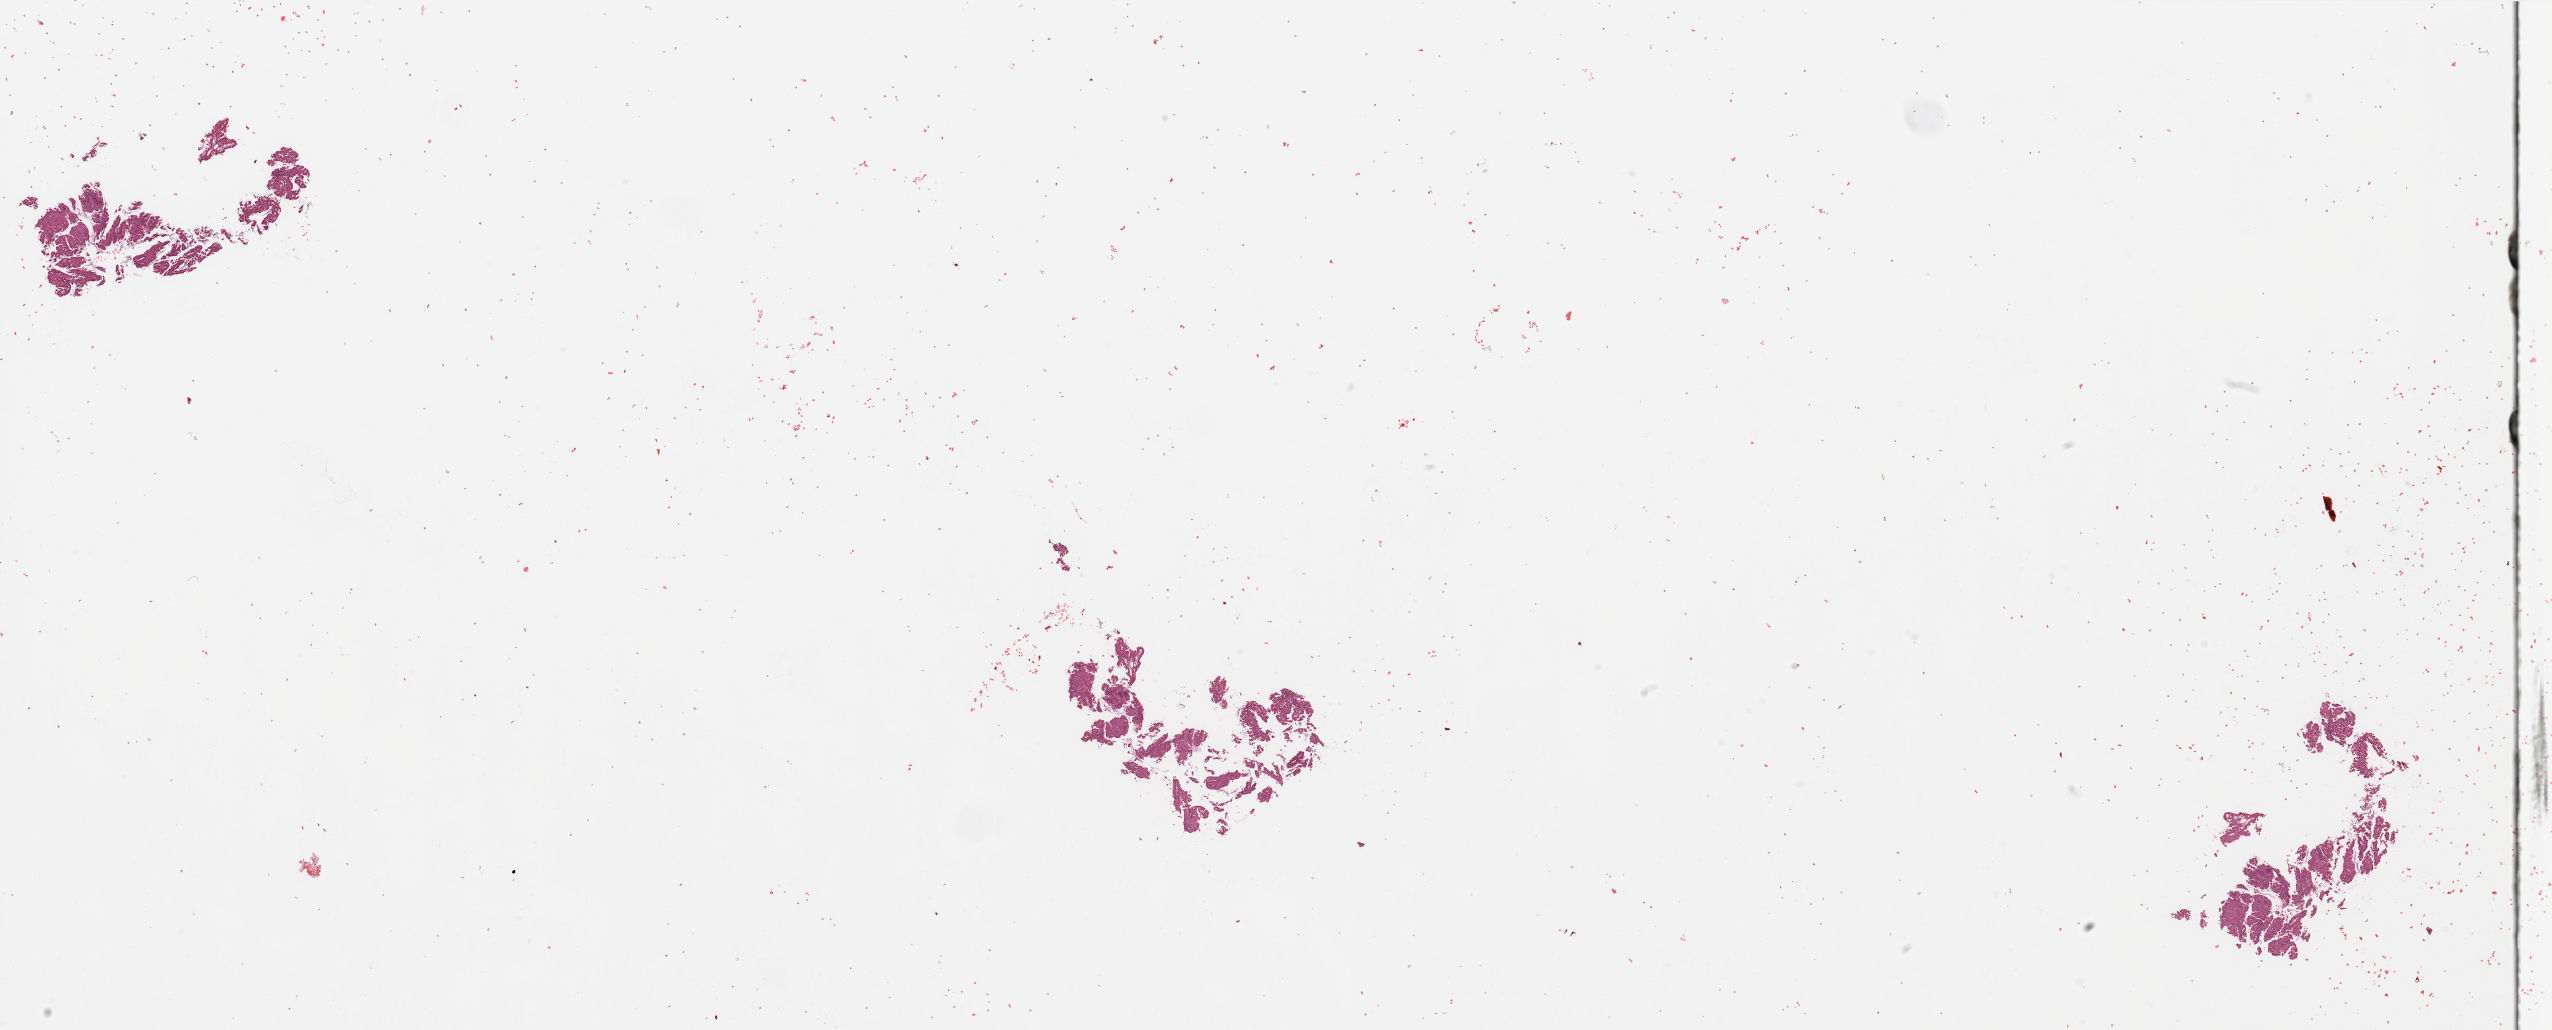
Whole-slide histology image, H&E, low-resolution overview of the scanned area, about 40.4 x 16.3 mm (acquisition: 20x scan), tumour tissue sample, sampled site: uterus. 58-year-old female patient. Histologic grade: G2 (moderately differentiated). Pathologist review of this section (percent, as recorded): tumour nuclei 90%, necrosis 5%.
* primary tumour site (as recorded): anterior endometrium
* histologic diagnosis: Endometrioid adenocarcinoma, NOS
* AJCC pathologic stage: I